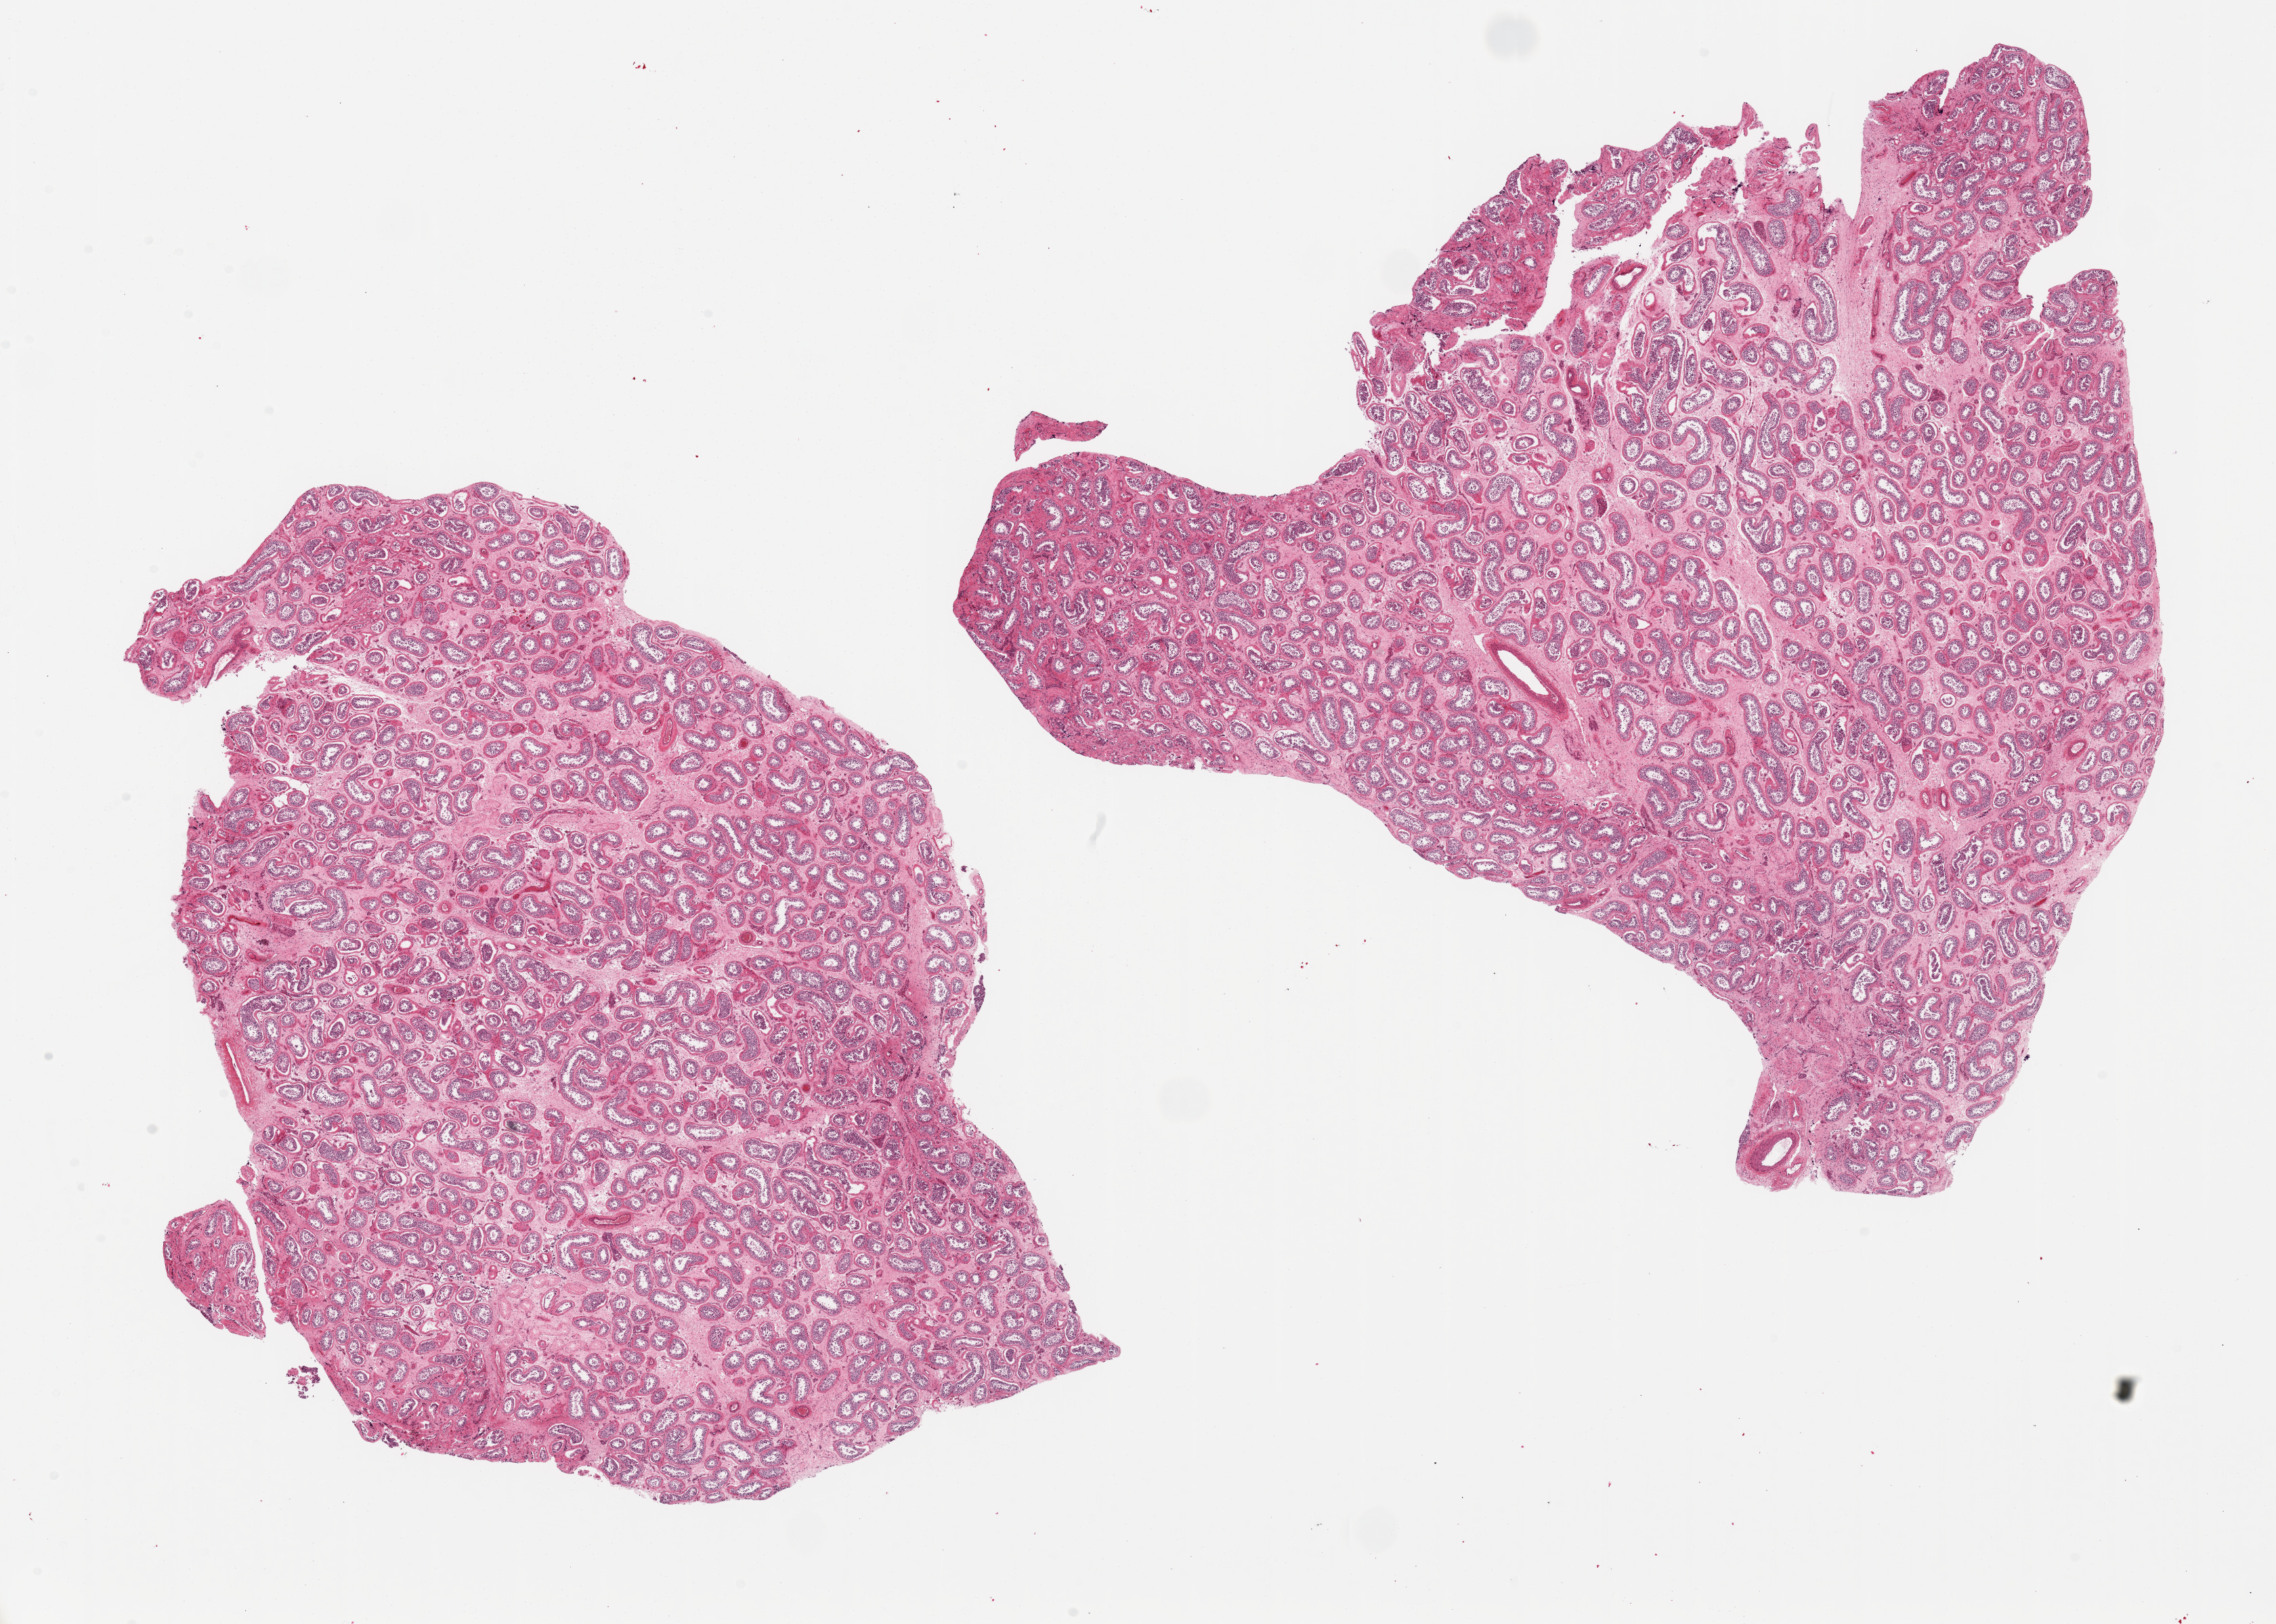
Whole-slide image, haematoxylin and eosin stain, low-resolution overview of the scanned area, about 26.6 x 19.0 mm (acquisition: 20x scan). PAXgene-fixed paraffin-embedded (PFPE) section. Target tissue: testis. Donor tissue sample.
• reviewer comment on this tissue sample: 2 pieces ~13x9mm. Spermatogenesis present, poorly preserved